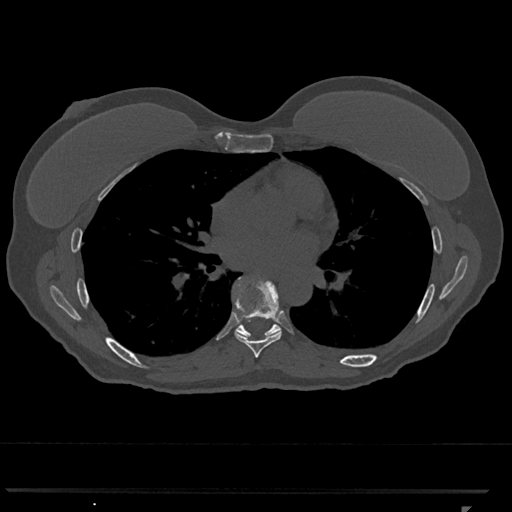
CT including the spine, one axial slice. Slice 697 of 793 in the series (ordered by position). Bone window (W 1800 / L 400 HU). 0.5 mm slice thickness. 512 × 512 image matrix, field of view 380 × 380 mm. Female patient, age 62 years. Case-level facts recorded for this patient, not image findings: primary cancer: renal.
Annotated regions visible in this slice (semi-automatic segmentation, software-assisted and operator-edited):
- T7 vertebra: box from (x=234, y=277) to (x=282, y=358) px
- T8 vertebra: (x=234, y=277)–(x=280, y=337)